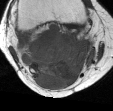
MRI of an extremity soft-tissue mass, one axial slice; slice 21 of 45 in the series (ordered by position); MR volume resampled by the dataset authors to the PET/CT grid (not the native acquisition matrix); 3.27 mm slice thickness; 113 × 111 image matrix, field of view 110 × 108 mm. Female patient. Case-level facts recorded for this patient, not image findings: histological type: liposarcoma; site of the primary tumour: right thigh.
Outlined on this slice (expert contour drawn on MRI and transferred to this co-registered scan by the dataset authors):
- gross tumour volume (mass): bounding box [x1, y1, x2, y2] px = [21, 24, 95, 89]